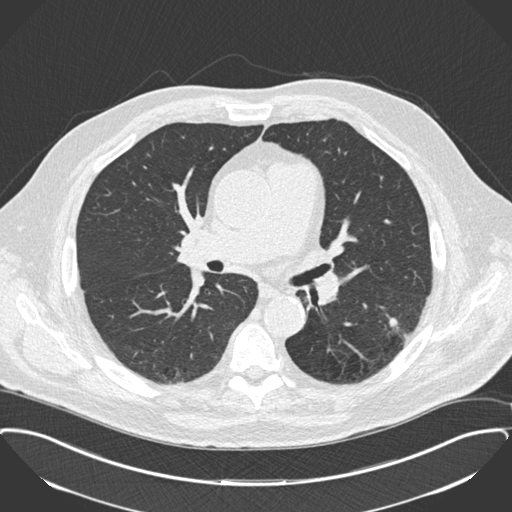
Low-dose screening chest CT, one axial slice. Slice 99 of 175 in the series (ordered by position). 120 kVp. Lung window (W 1500 / L -600 HU). 2 mm slice thickness. 512 × 512 image matrix, field of view 400 × 400 mm.
Structures marked on this image (expert manual segmentation):
- lesion 1 (tumor, lower lobe of left lung): bounding box <387,315,409,340> (left, top, right, bottom; pixels)